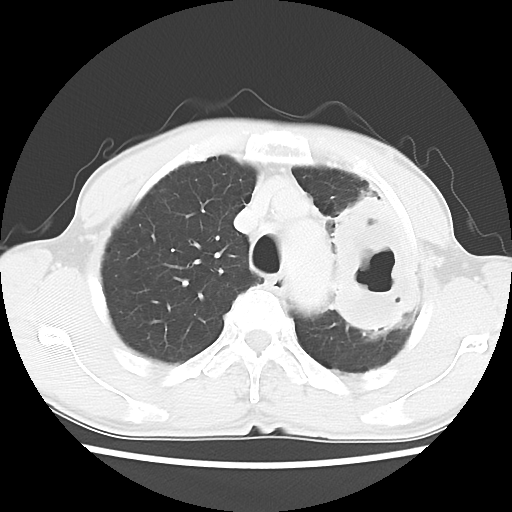
Chest CT, one axial slice; position 46 of 60 along the scan axis; reconstruction kernel LUNG; lung window (W 1500 / L -600 HU); 512 × 512 image matrix. Patient: male, 64 years. Case-level facts recorded for this patient, not image findings: clinical TNM (as recorded): T3 N3 M0; histopathological grade: G3.
Outlined on this slice (rectangle marked by the reading radiologist):
- lung tumour (recorded histology: adenocarcinoma): bounding box <319,189,425,342> (left, top, right, bottom; pixels)